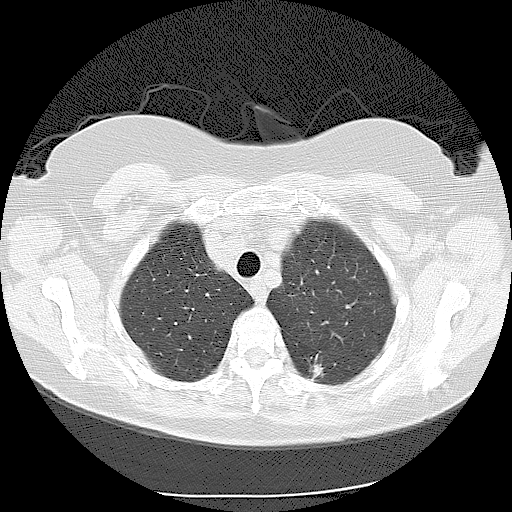
Low-dose screening chest CT, one axial slice. Reconstruction kernel LUNG. Lung window (W 1500 / L -600 HU). 2.5 mm slice thickness. 512 × 512 image matrix, field of view 360 × 360 mm.
Annotated regions visible in this slice (expert manual segmentation):
- lesion 1 (tumor, lower lobe of left lung): bounding box (x1, y1, x2, y2) in pixels: (311, 364, 324, 380)